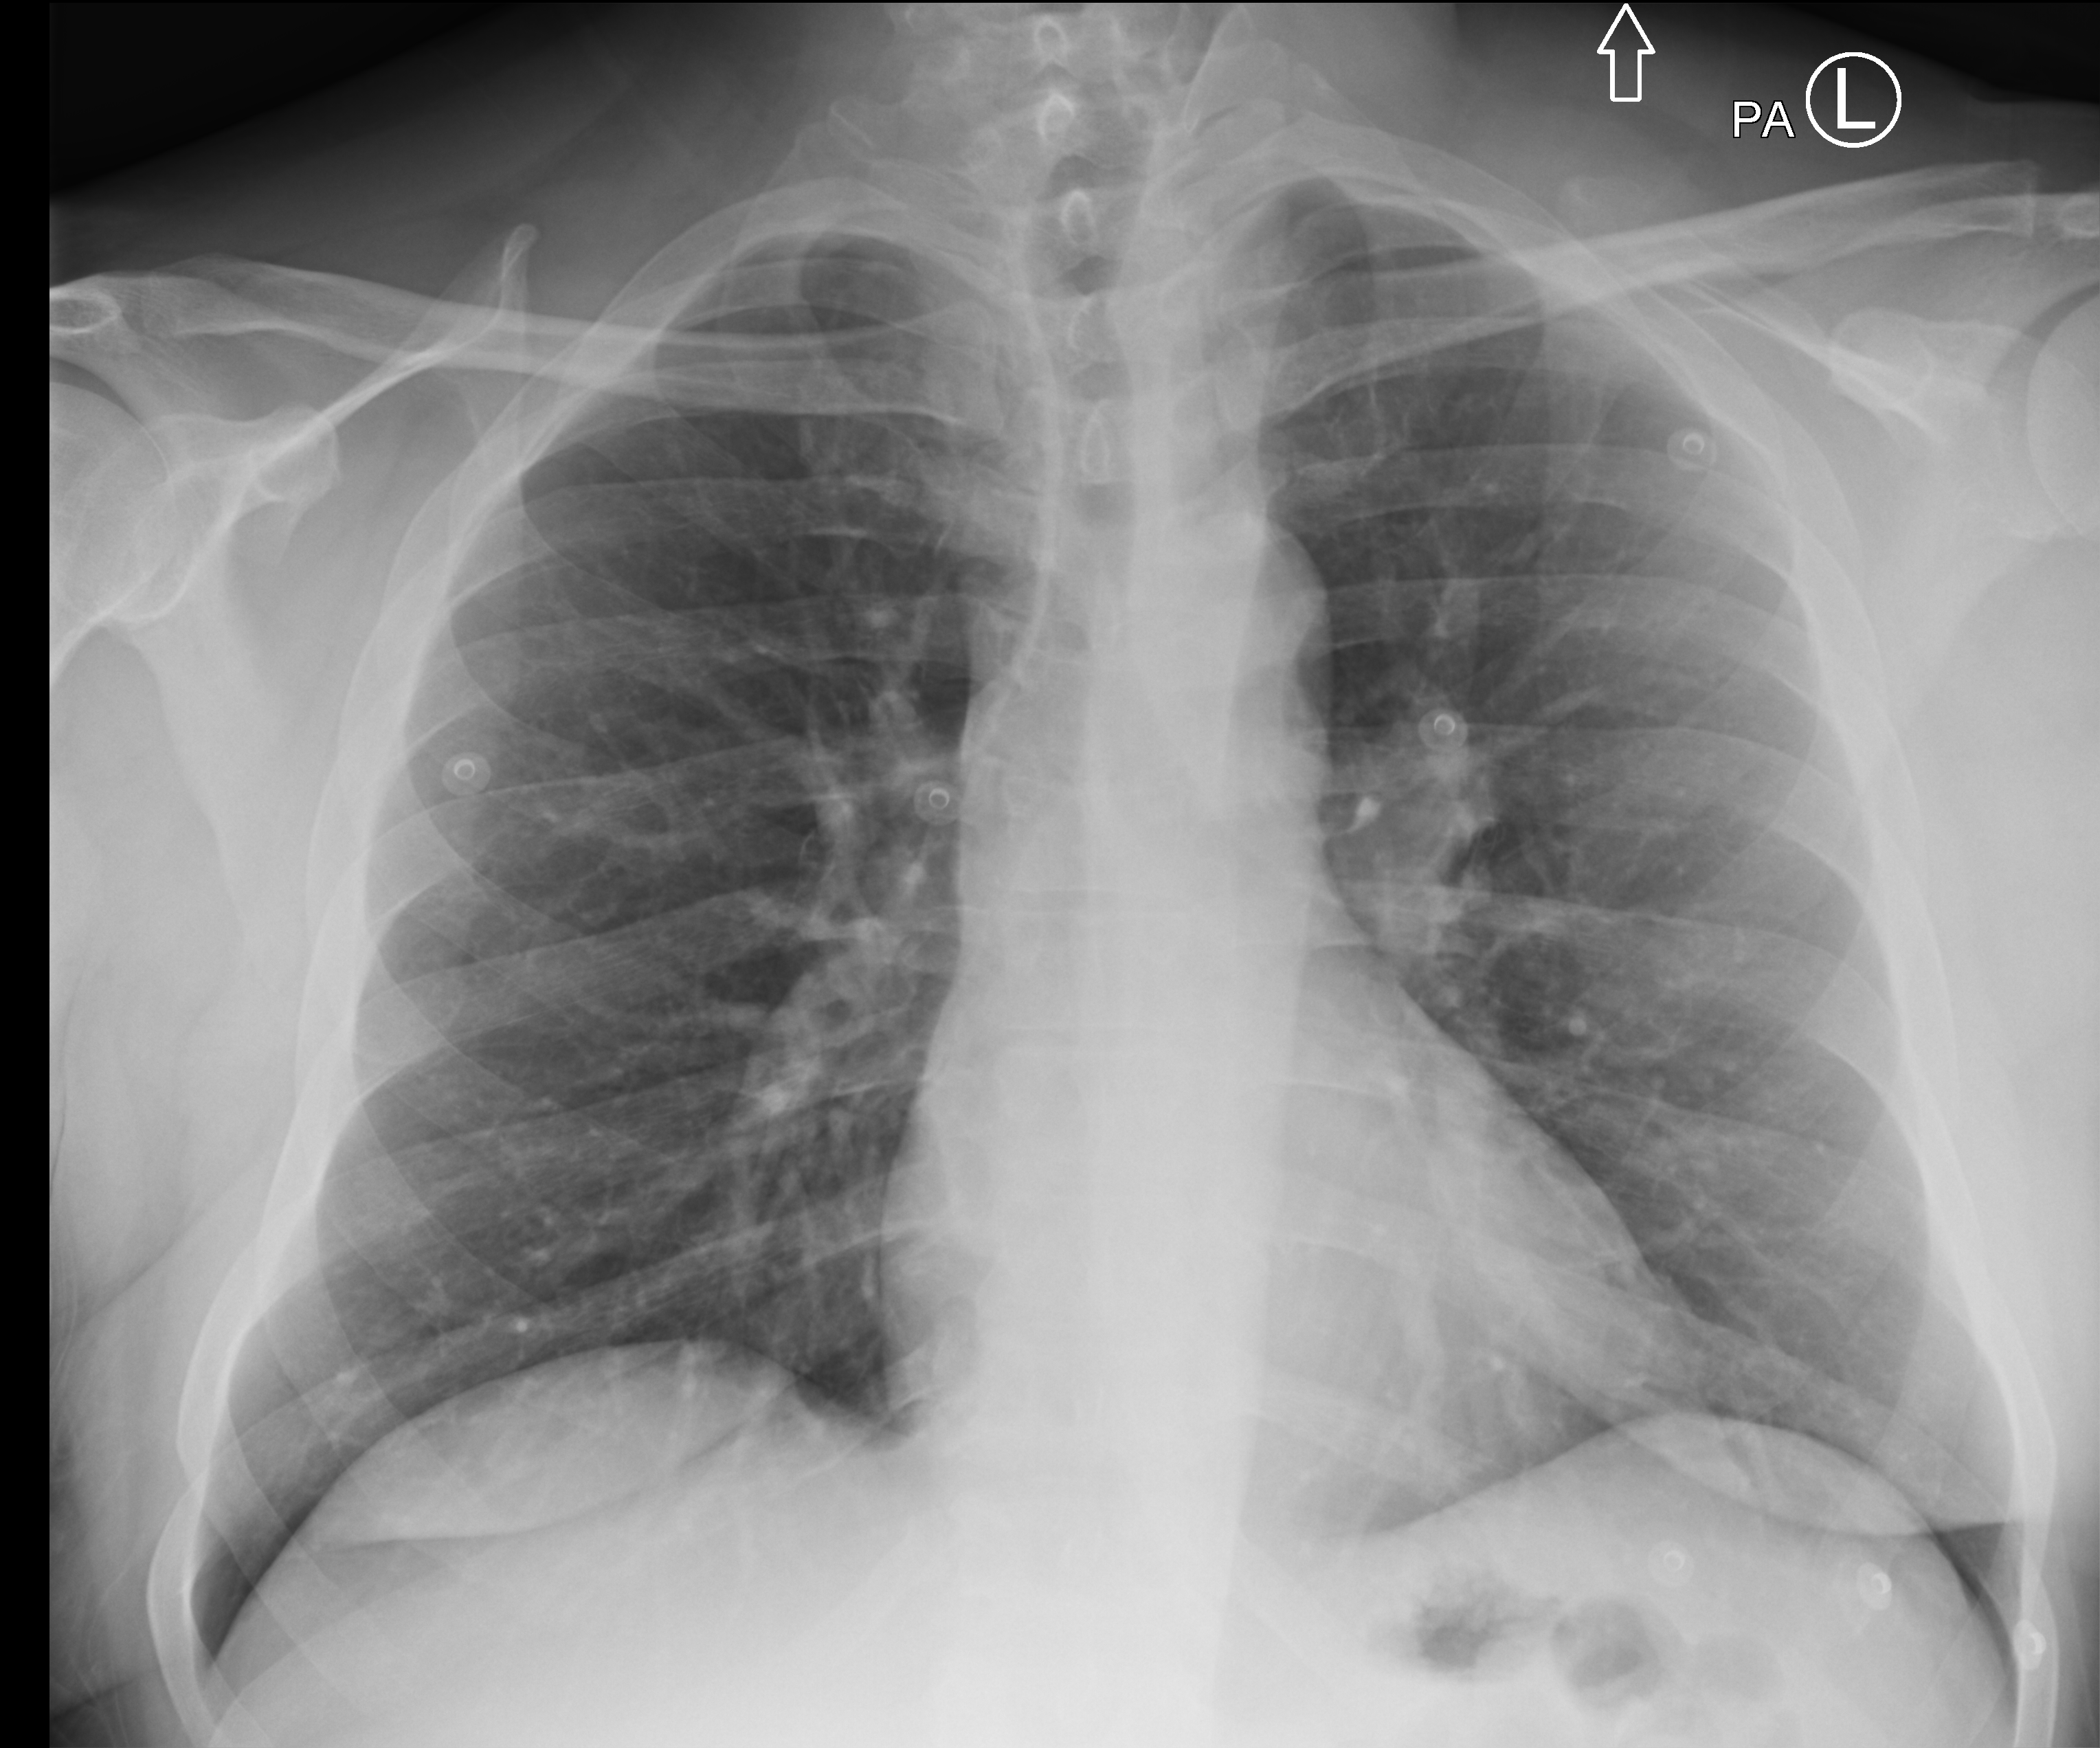
Chest X-ray, posteroanterior (PA) projection. Patient hospitalised with COVID-19; male, aged 18–59 years.
From the hospital-stay record, not from the radiograph (when in the stay this image was taken is not recorded): admitted to intensive care during this hospital stay: no.